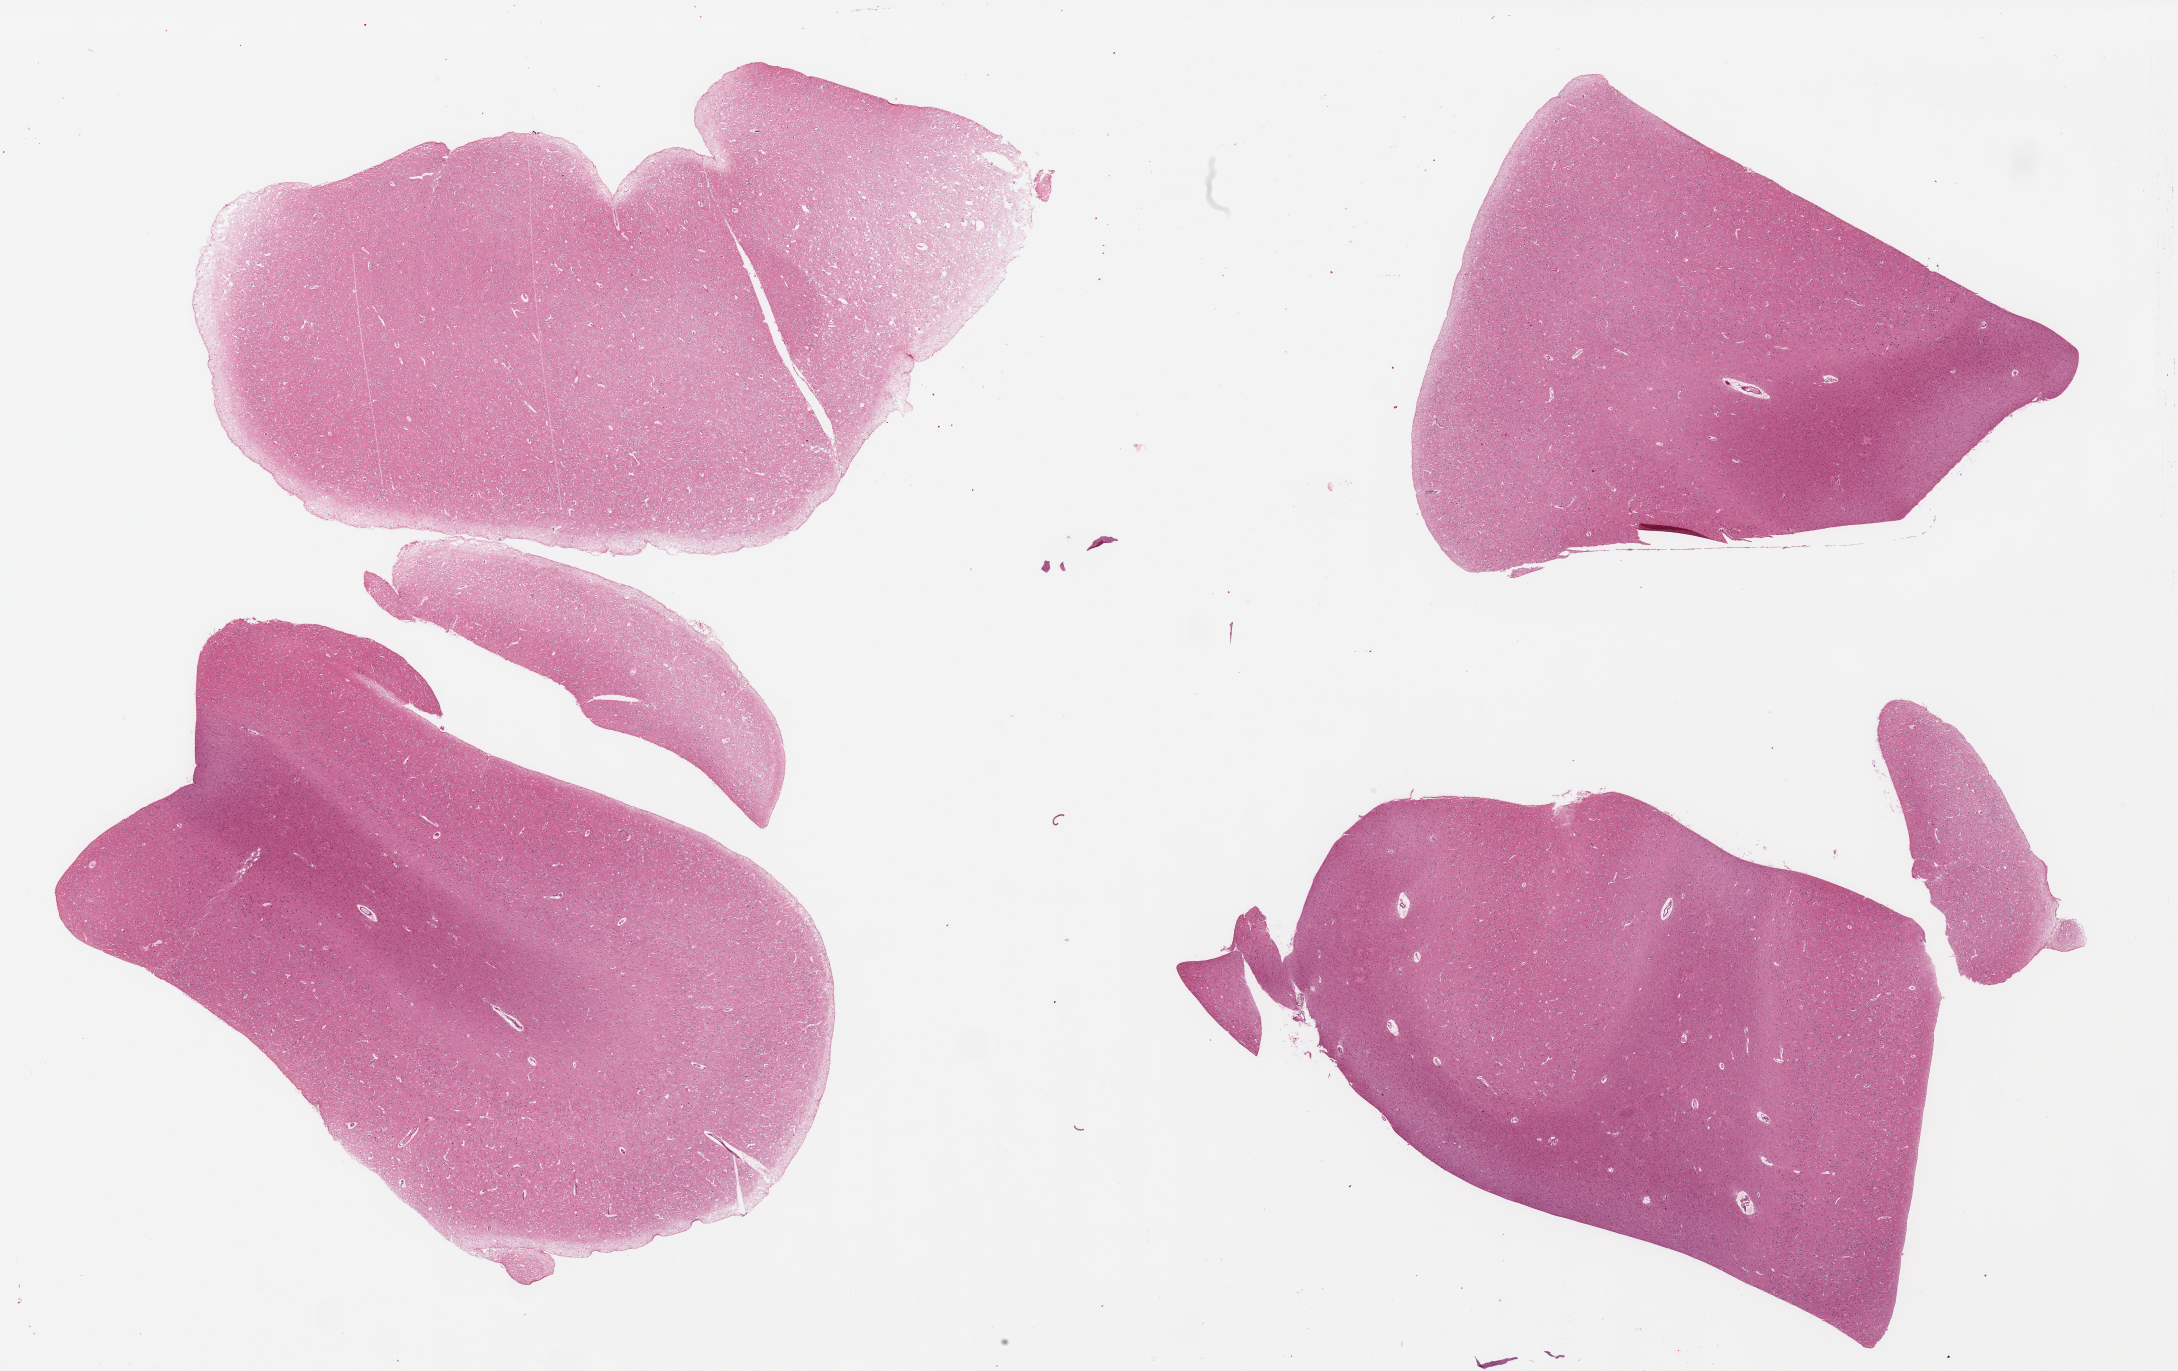
Whole-slide image, haematoxylin and eosin stain, brightfield — a low-resolution overview of the entire scanned area, about 34.5 x 21.7 mm. PAXgene-fixed, paraffin-embedded tissue. Section of cerebral cortex (target tissue). Tissue donor sample. Donor: male.
* review note (as recorded): 4 pieces, no abnormalities